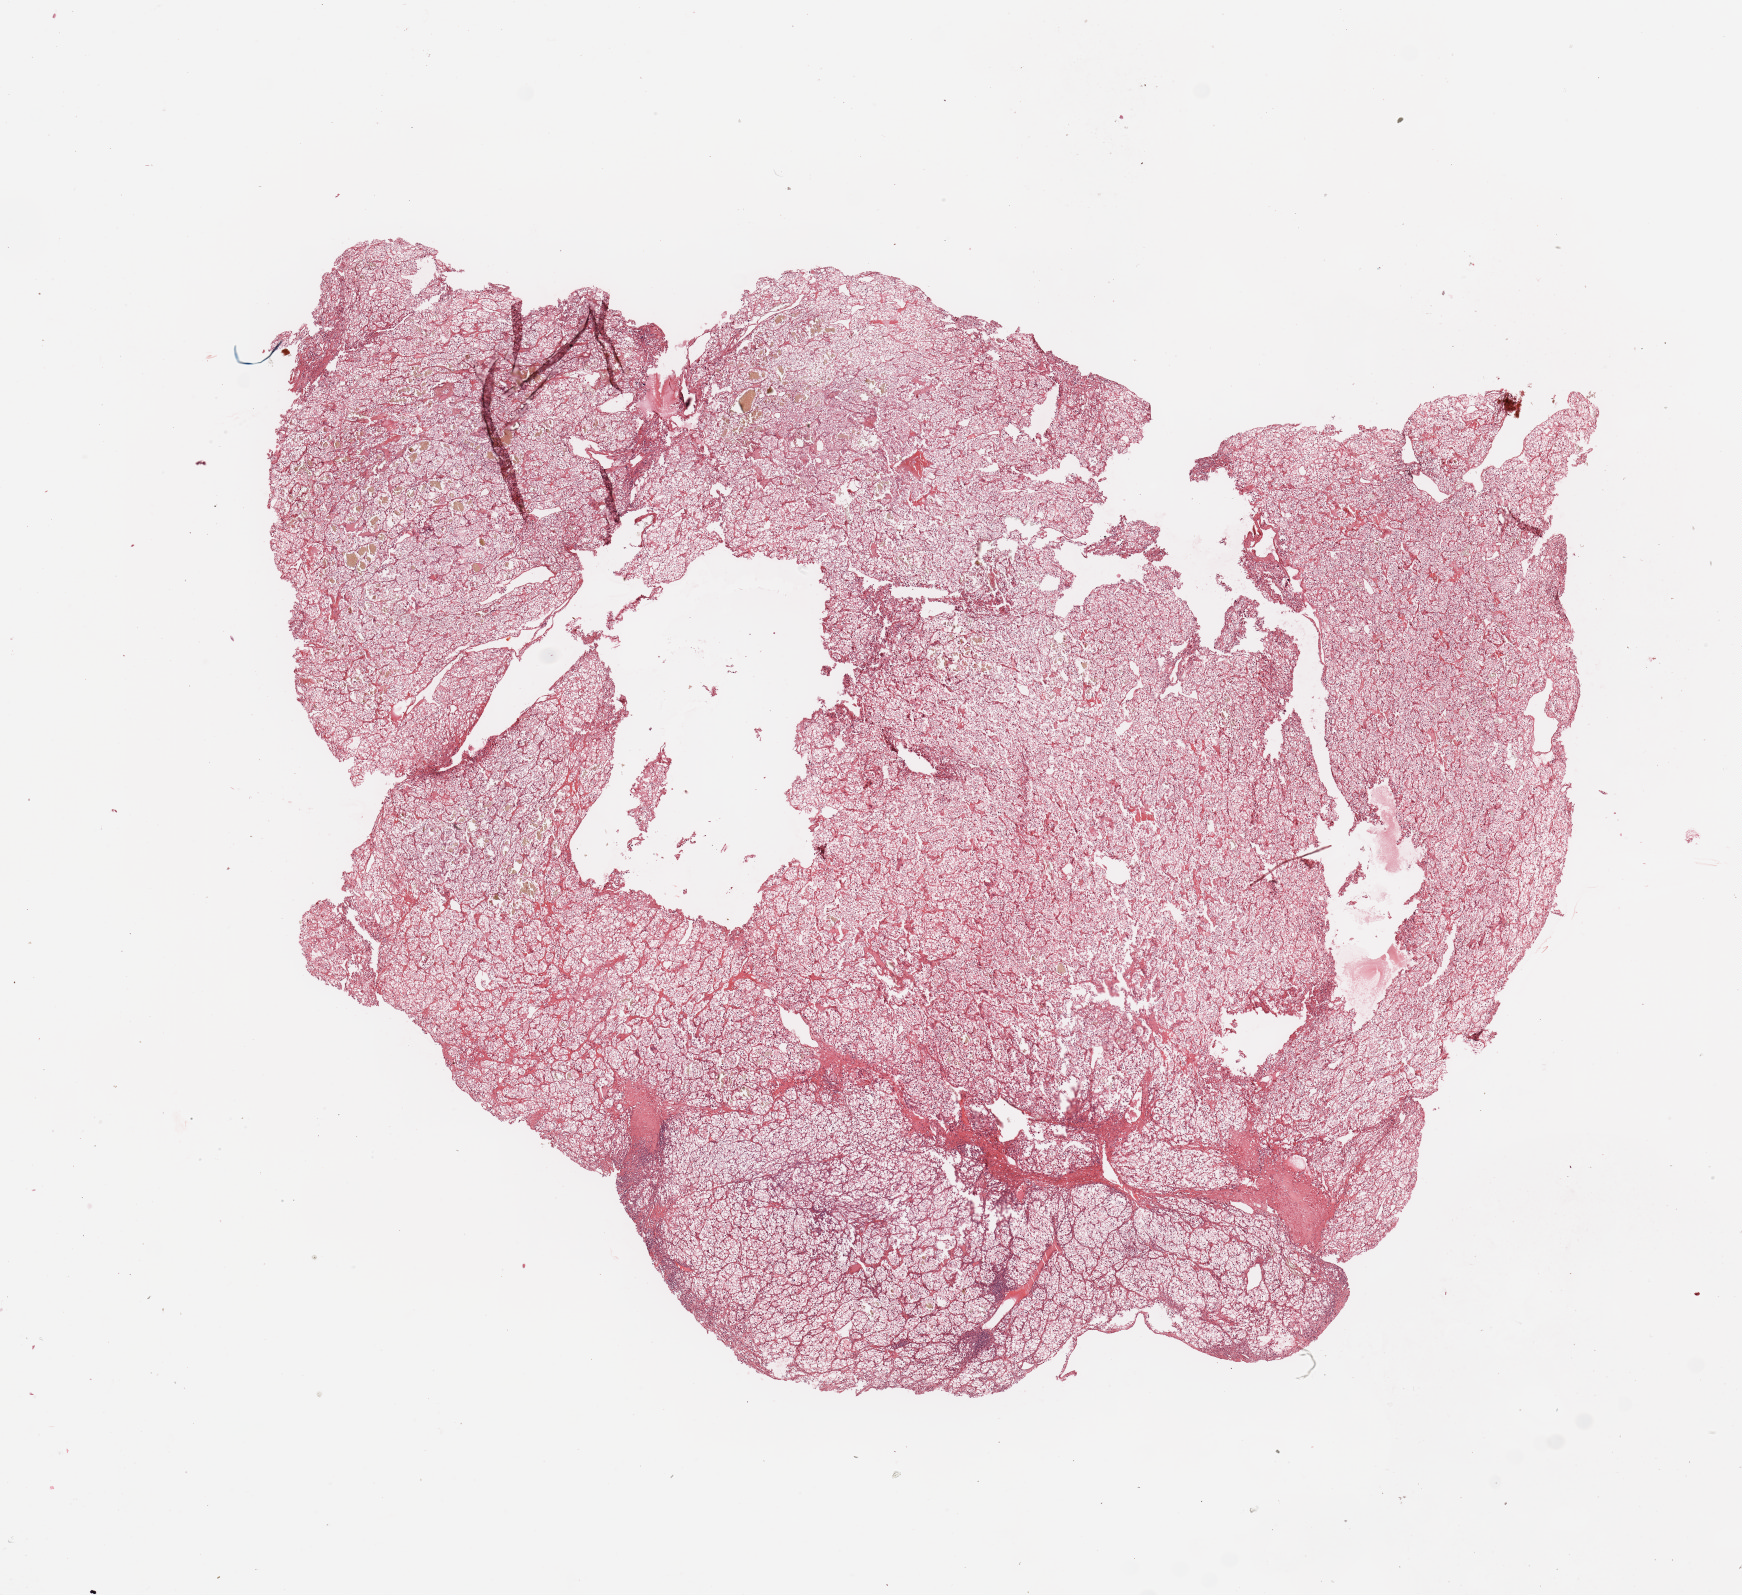
Digitized H&E-stained tissue section (whole slide), shown as a low-resolution overview of the whole scanned area (about 13.8 x 12.6 mm, slide scanned at 20x); kidney, tumour tissue. Male, 65 y/o. Histologic grade: G2 (moderately differentiated).
- primary tumour site (as recorded): upper pole
- diagnosis: Renal cell carcinoma, NOS
- AJCC pathologic stage: III